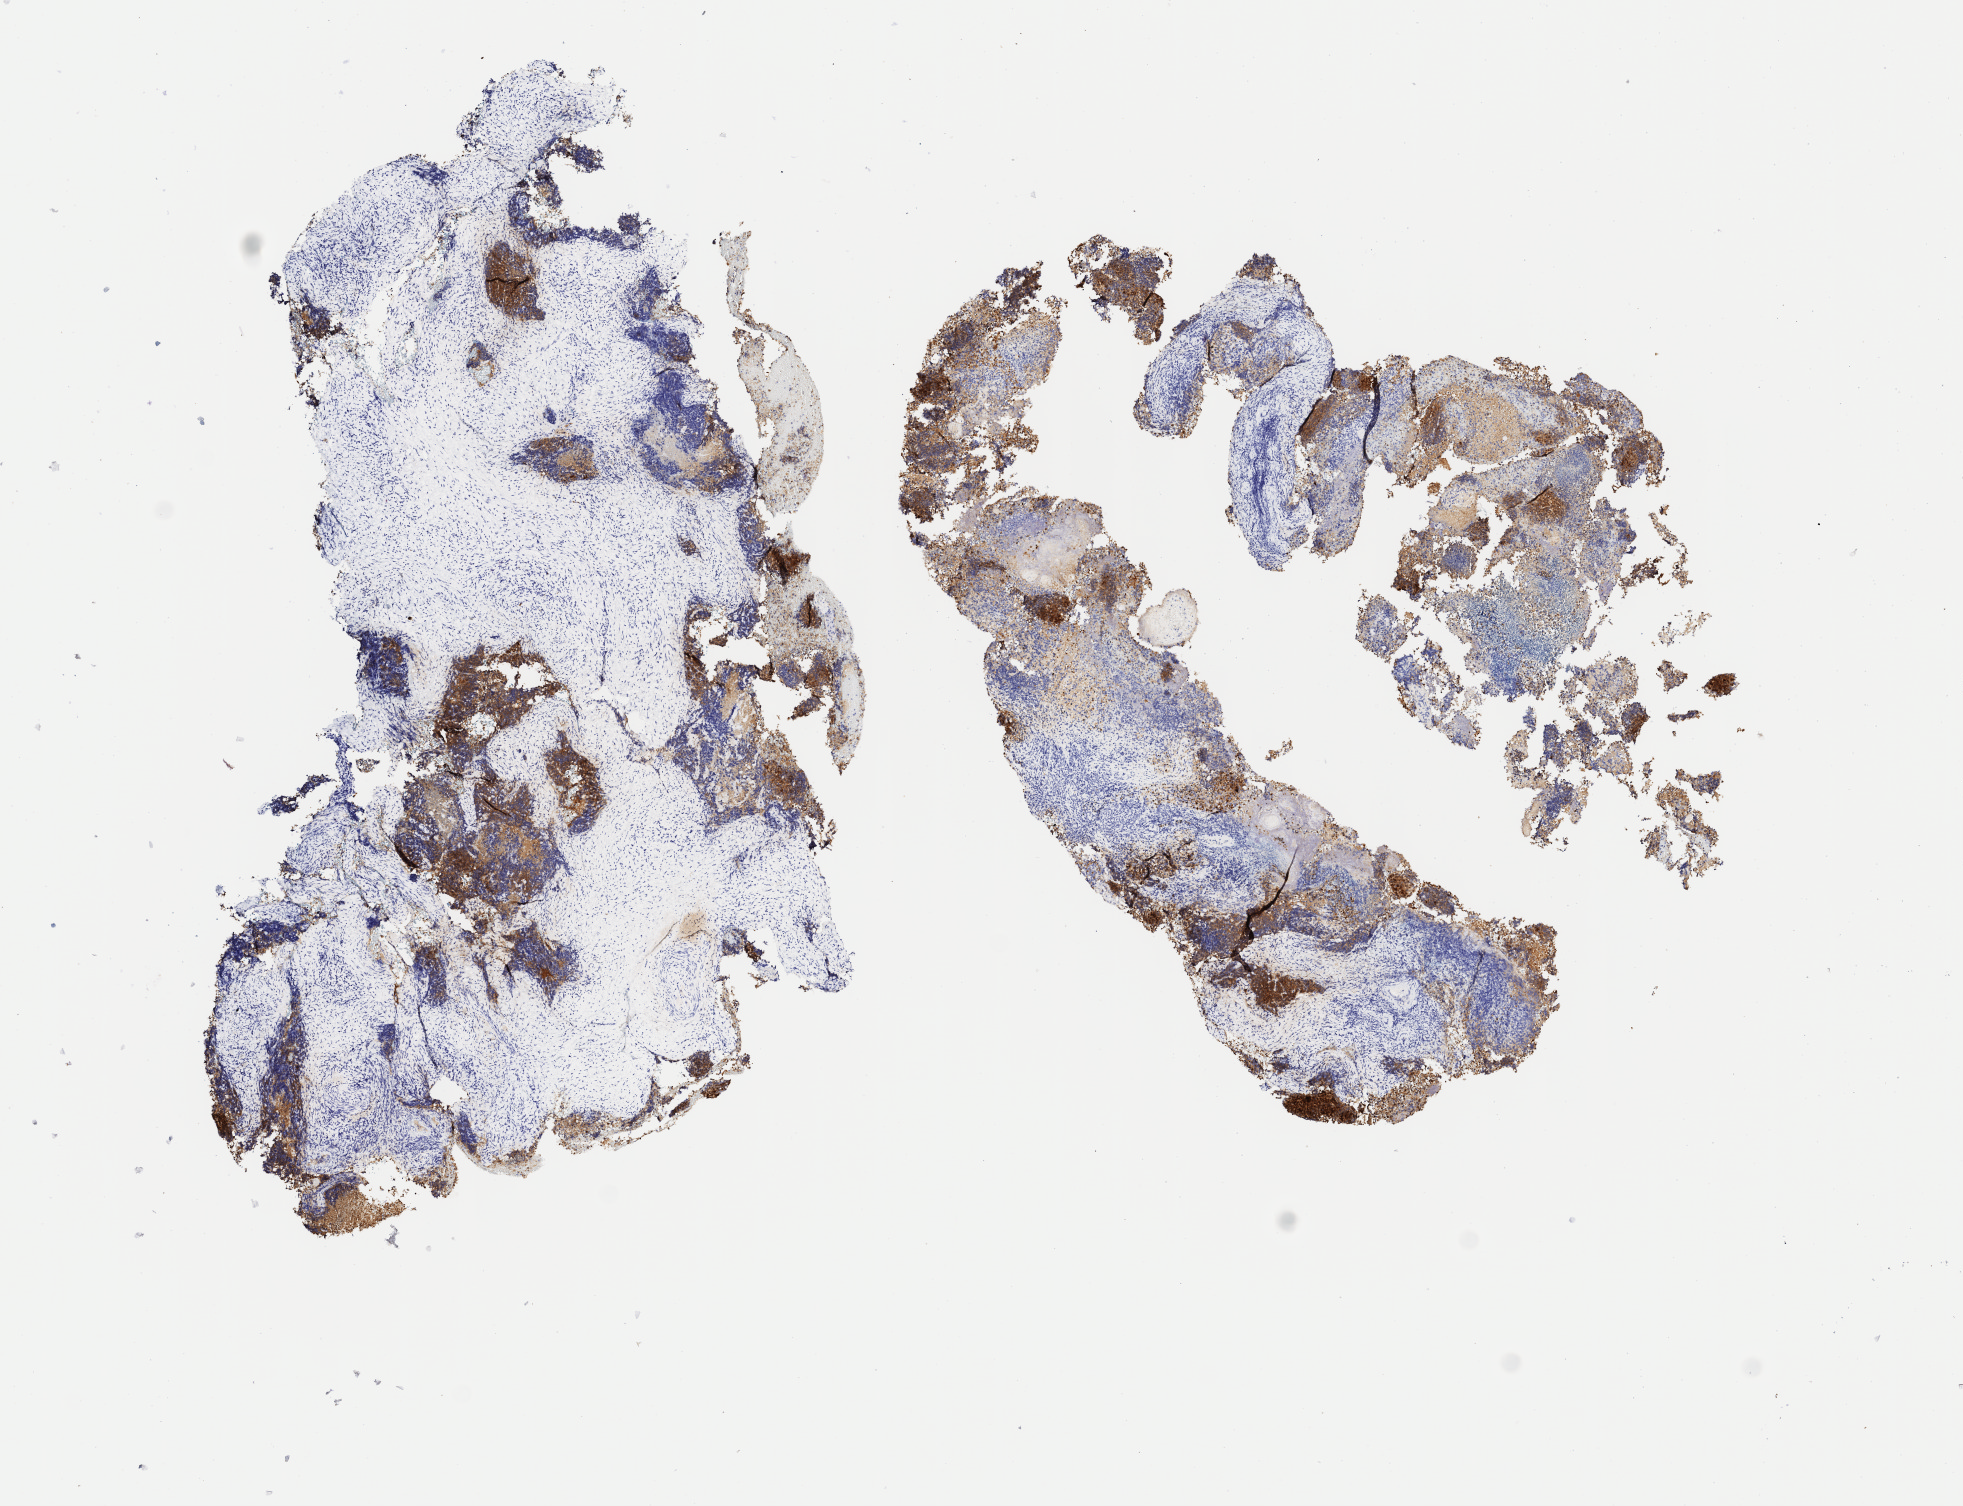
IHC for p16 (p16INK4a), whole-slide image — shown as a low-resolution overview of the whole scanned area (about 7.8 x 6.0 mm); specimen: tumor tissue; site: cervix. Patient: female, aged 47.
Diagnosis: Squamous cell carcinoma, large cell, nonkeratinizing, NOS.